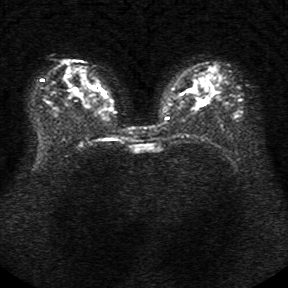
Breast MRI, one axial slice; position 20 of 34 along the scan axis; diffusion-weighted series; image 2 of 4 stored at this slice position (different b-values; order by instance number); 1.5 T; 5 mm slice thickness; 288 × 288 image matrix. Female patient.
Annotated regions visible in this slice (manually delineated by an expert):
- tumour on diffusion-weighted imaging: box from (x=196, y=100) to (x=205, y=107) px